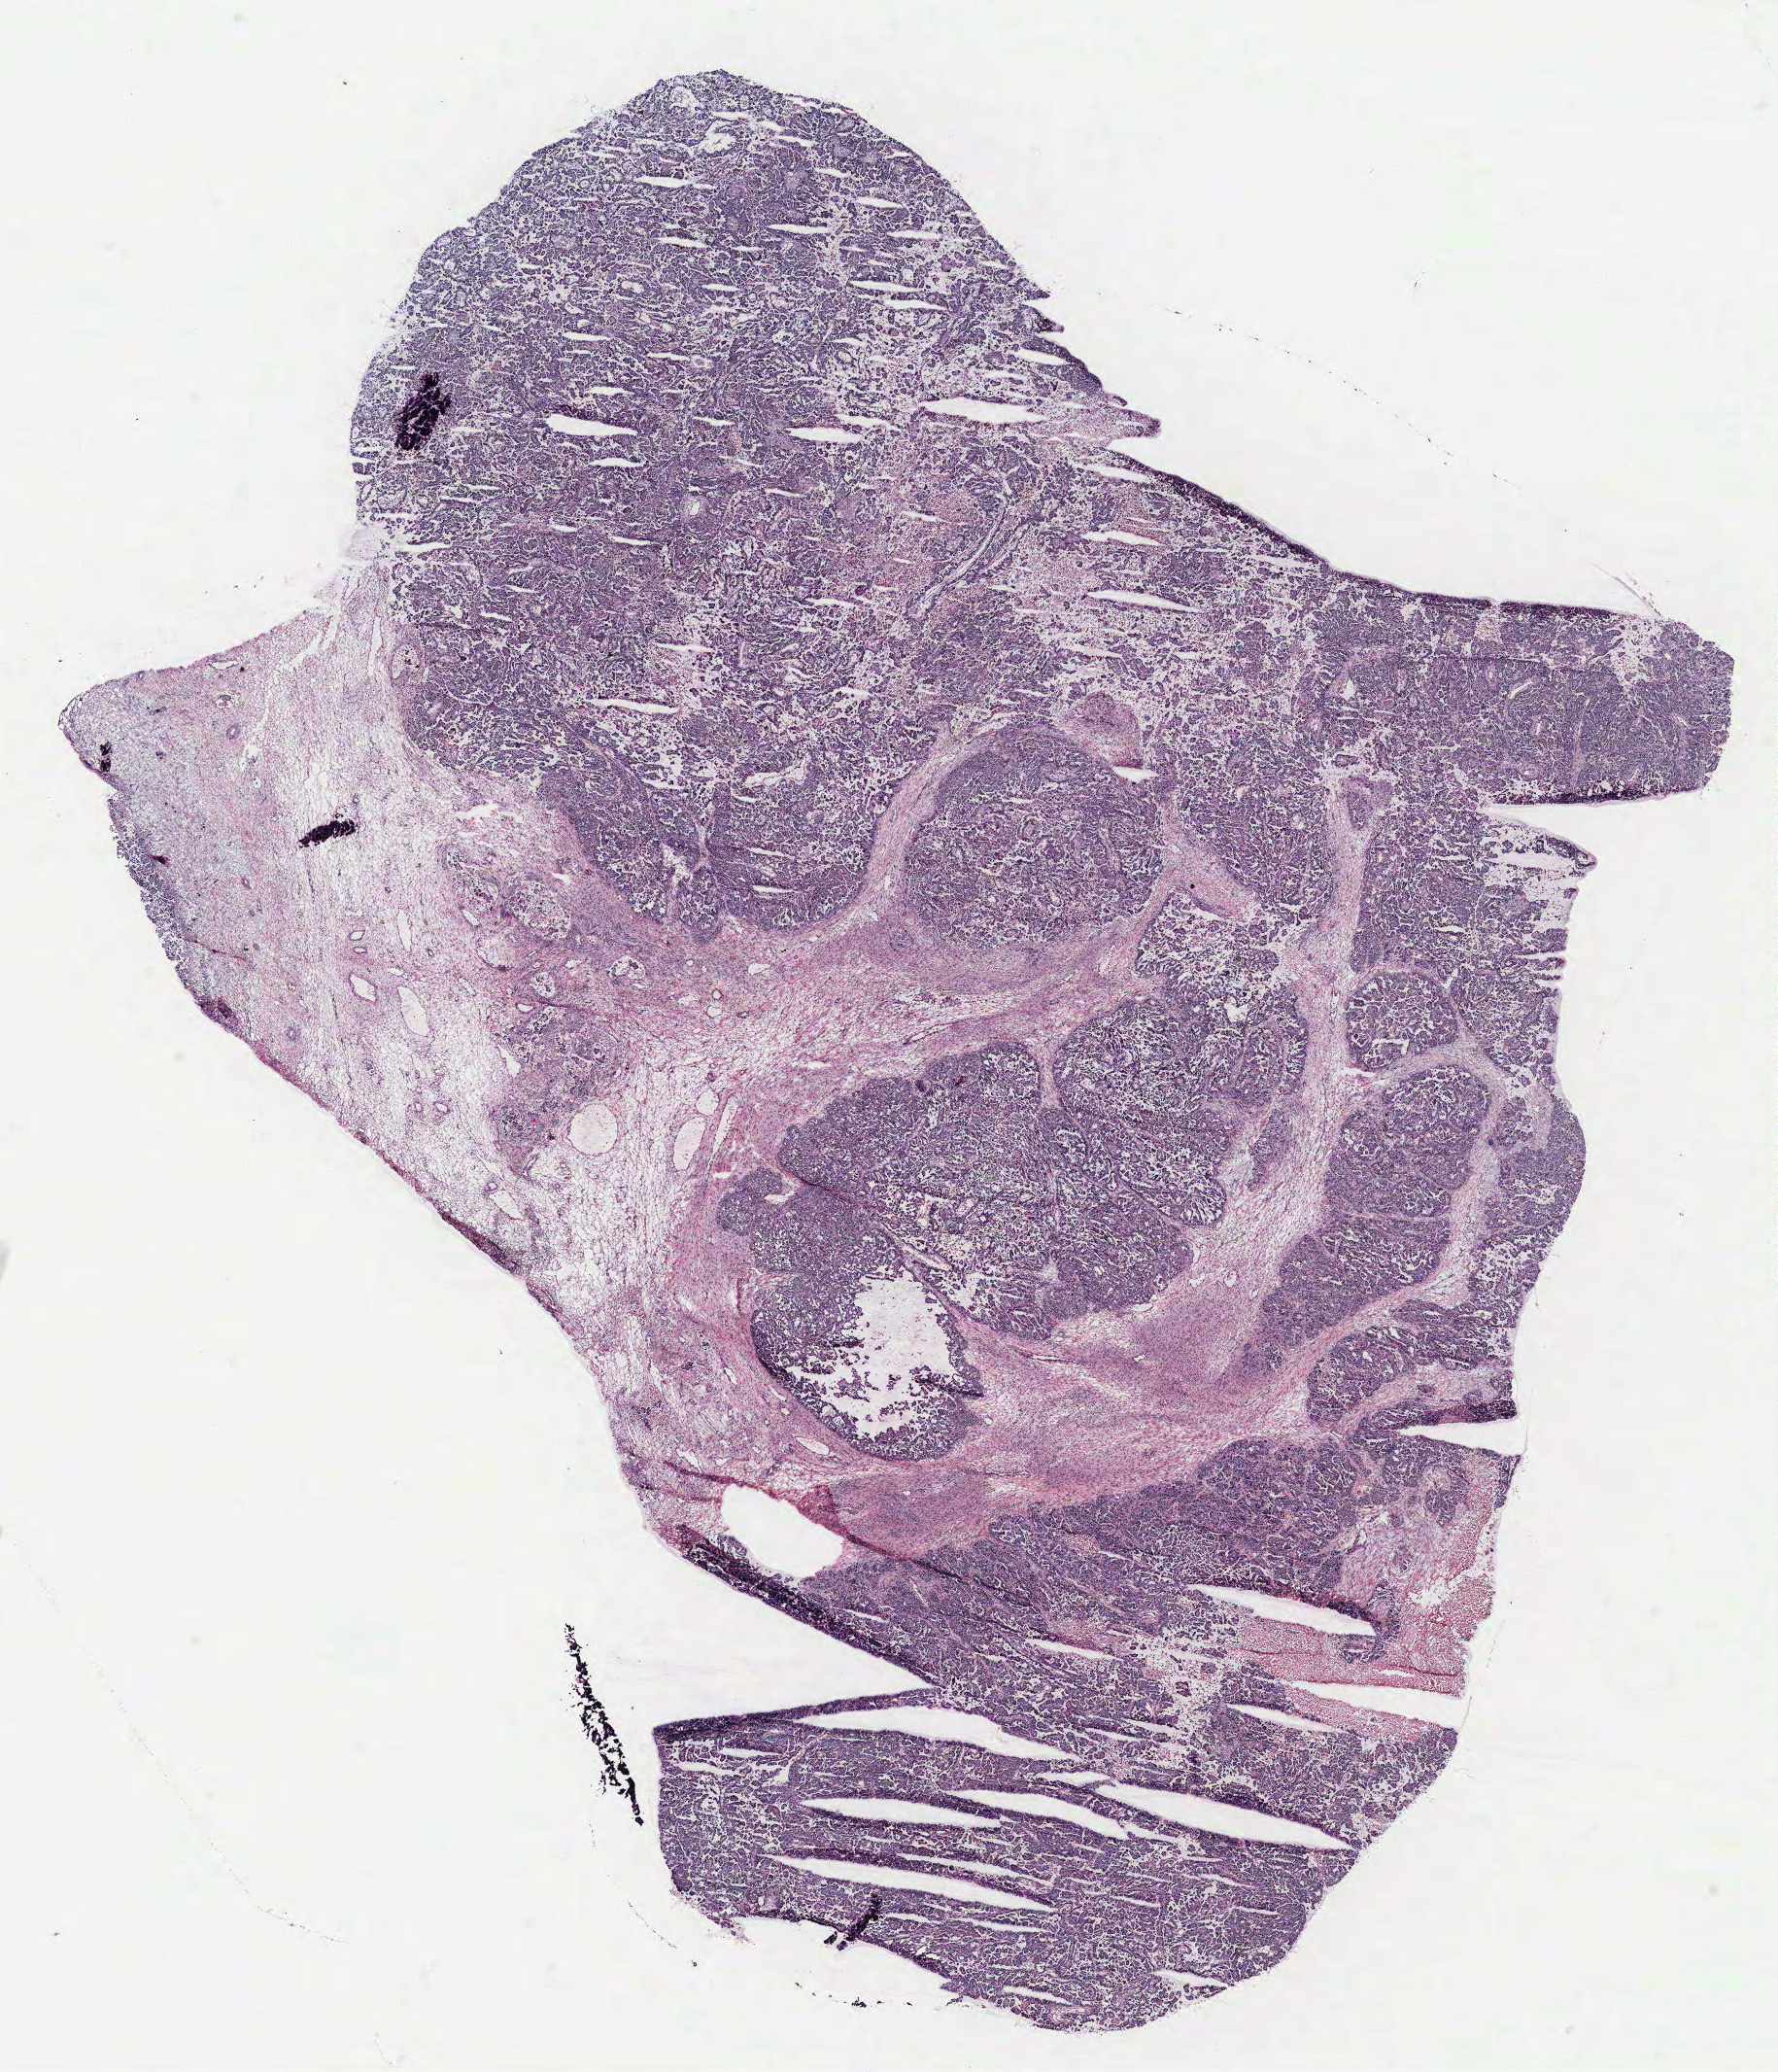
Whole-slide histology image, H&E-stained — a low-resolution overview of the entire scanned area, about 14.6 x 17.1 mm (acquisition: 40x scan), ovary, tumour tissue. Patient: female, age 56 years.
Diagnosis: Serous adenocarcinoma, NOS. Primary tumour site (as recorded): ovary.